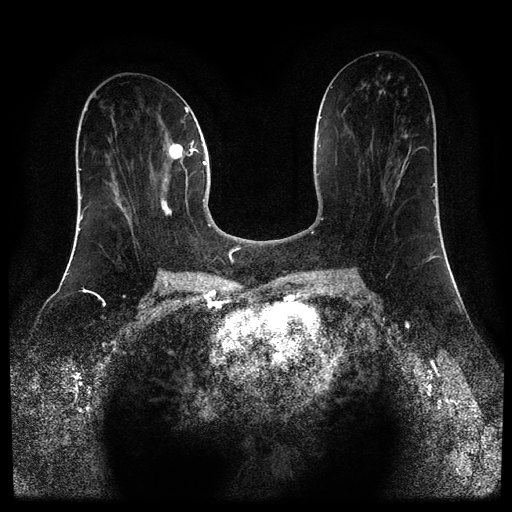
Breast MRI (dynamic contrast-enhanced, multi-phase), one axial slice; slice 40 of 110 in the series (ordered by position); dynamic contrast-enhanced series, time point 2 of 5 at this slice position (early post-contrast); 1.5 T; TE 2.6 ms, TR 5.4 ms; 2 mm slice thickness; 512 × 512 image matrix, field of view 340 × 340 mm. Female patient, age 43 years.
Structures marked on this image (semi-automatically segmented with operator editing):
- breast lesion (labelled 'tumour' in the annotation; benign lesions carry a separate 'benign' label): bounding box (x1, y1, x2, y2) in pixels: (160, 143, 184, 216)